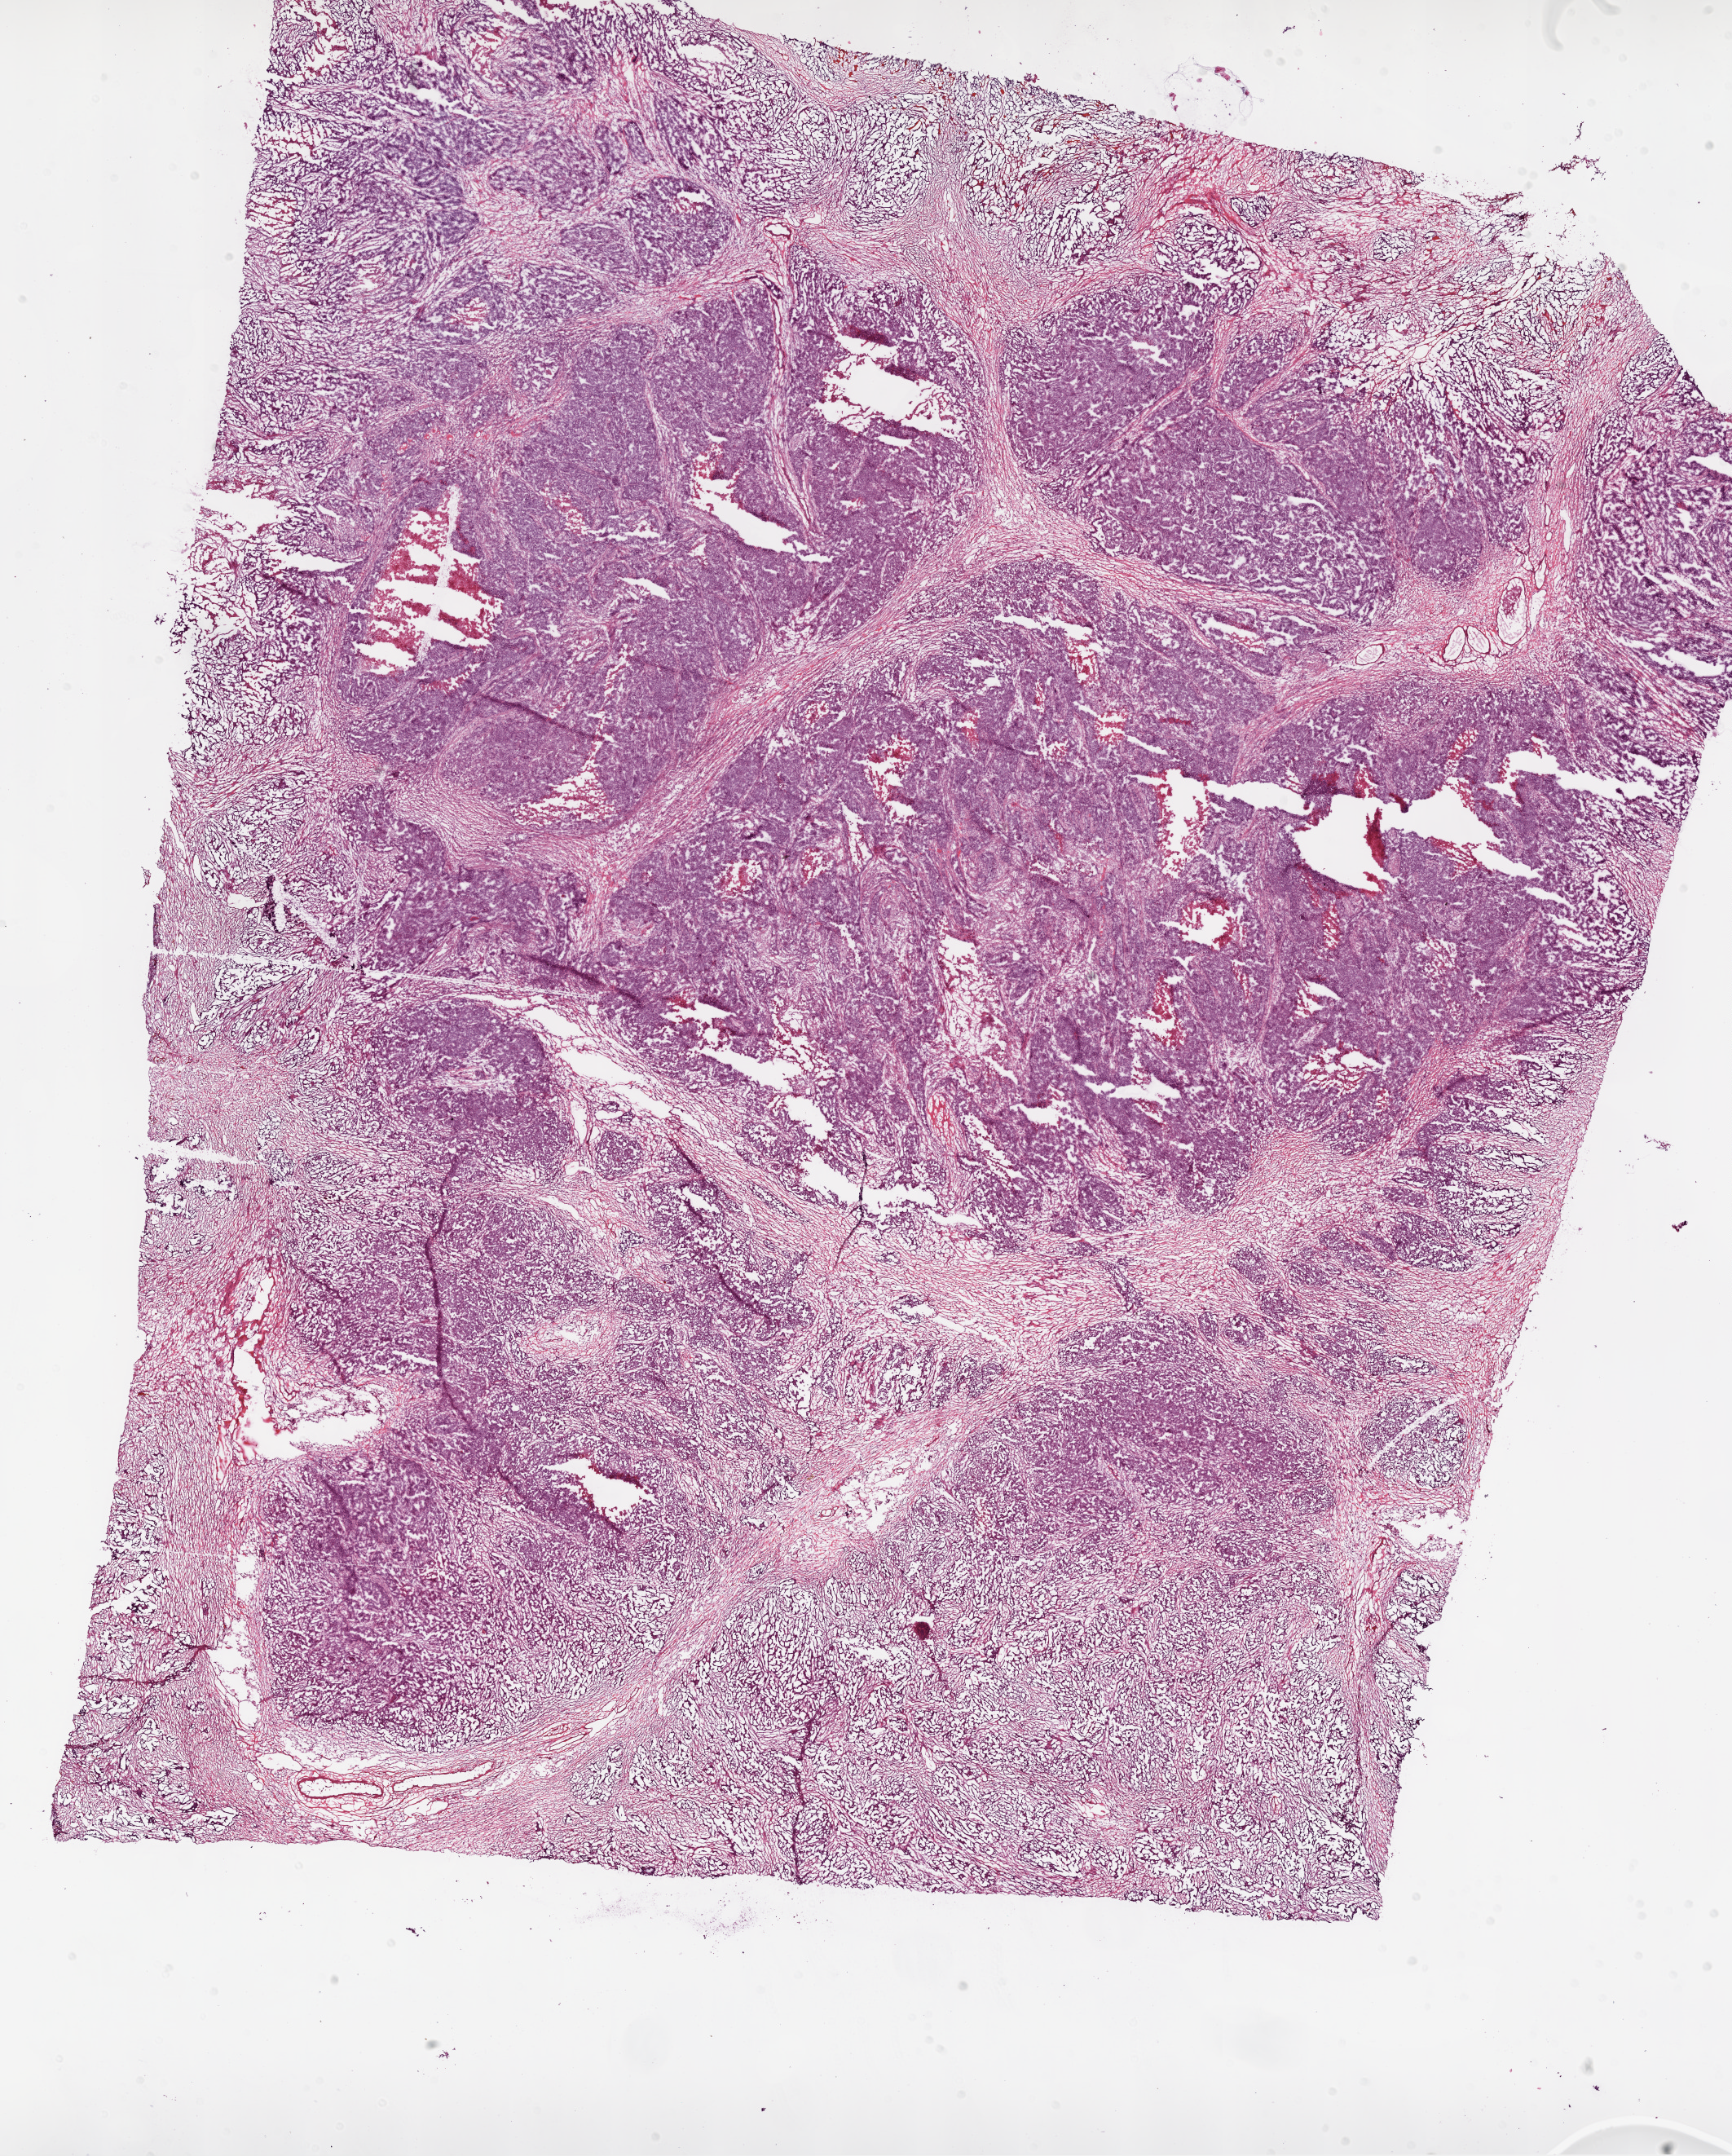
Digitized H&E tissue section (whole slide) — a low-resolution overview of the entire scanned area, about 17.1 x 21.2 mm (slide scanned at 20x), frozen section from the bottom of the tissue portion, primary tumour sample from the ovary. Female patient; age at initial diagnosis 64 years. Histologic grade: G3 (poorly differentiated). Slide review estimates, as recorded: tumour cells 85%, tumour nuclei 90%, normal cells 0%, stromal cells 10%, necrosis 5%.
FIGO stage: IV. Pathologic diagnosis: Serous cystadenocarcinoma, NOS. Laterality: bilateral.